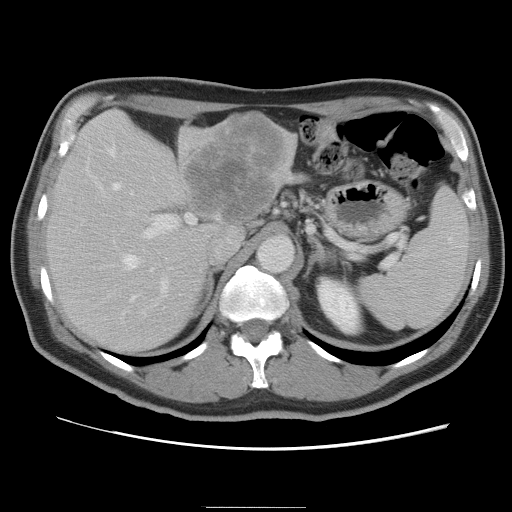
Contrast-enhanced abdominal CT, one axial slice. Slice 53 of 87 in the series (ordered by position). 120 kVp. Intravenous contrast given. Soft-tissue window (W 400 / L 40 HU). 5 mm slice thickness. 512 × 512 image matrix. Male patient, age 63 years. From the clinical record (not read from this slice): diagnosis: colorectal cancer liver metastases, imaged before liver resection; multiple liver metastases: no; largest metastasis: 9 cm.
Annotated regions visible in this slice (expert manual segmentation):
- hepatic veins: box from (x=109, y=149) to (x=154, y=302) px
- liver: (x=46, y=113)–(x=297, y=354)
- planned liver remnant (the part of the liver to remain after resection): (x=46, y=147)–(x=208, y=355)
- portal vein (with intrahepatic branches): (x=96, y=181)–(x=196, y=315)
- liver metastasis: (x=185, y=118)–(x=284, y=227)